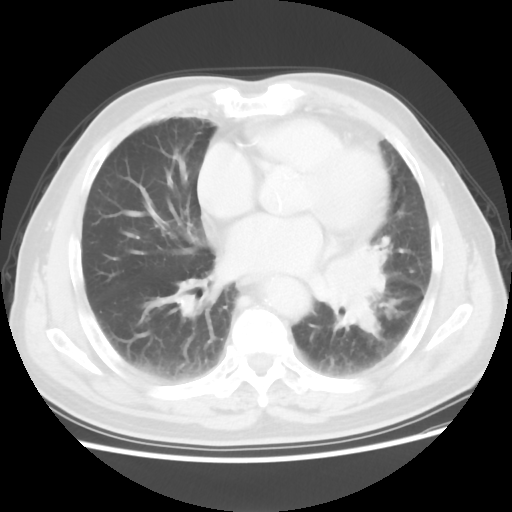
Chest CT, one axial slice. Slice 27 of 56 in the series (ordered by position). Reconstruction kernel STANDARD. 120 kVp. Lung window (W 1500 / L -600 HU). 5 mm slice thickness. 512 × 512 image matrix. Patient: male, 75 years. From the clinical record (not read from this slice): clinical TNM (as recorded): T3 N0 M0.
Annotated regions visible in this slice (bounding box drawn by a radiologist):
- lung tumour (recorded histology: squamous cell carcinoma): bounding box (x1, y1, x2, y2) in pixels: (313, 240, 396, 343)